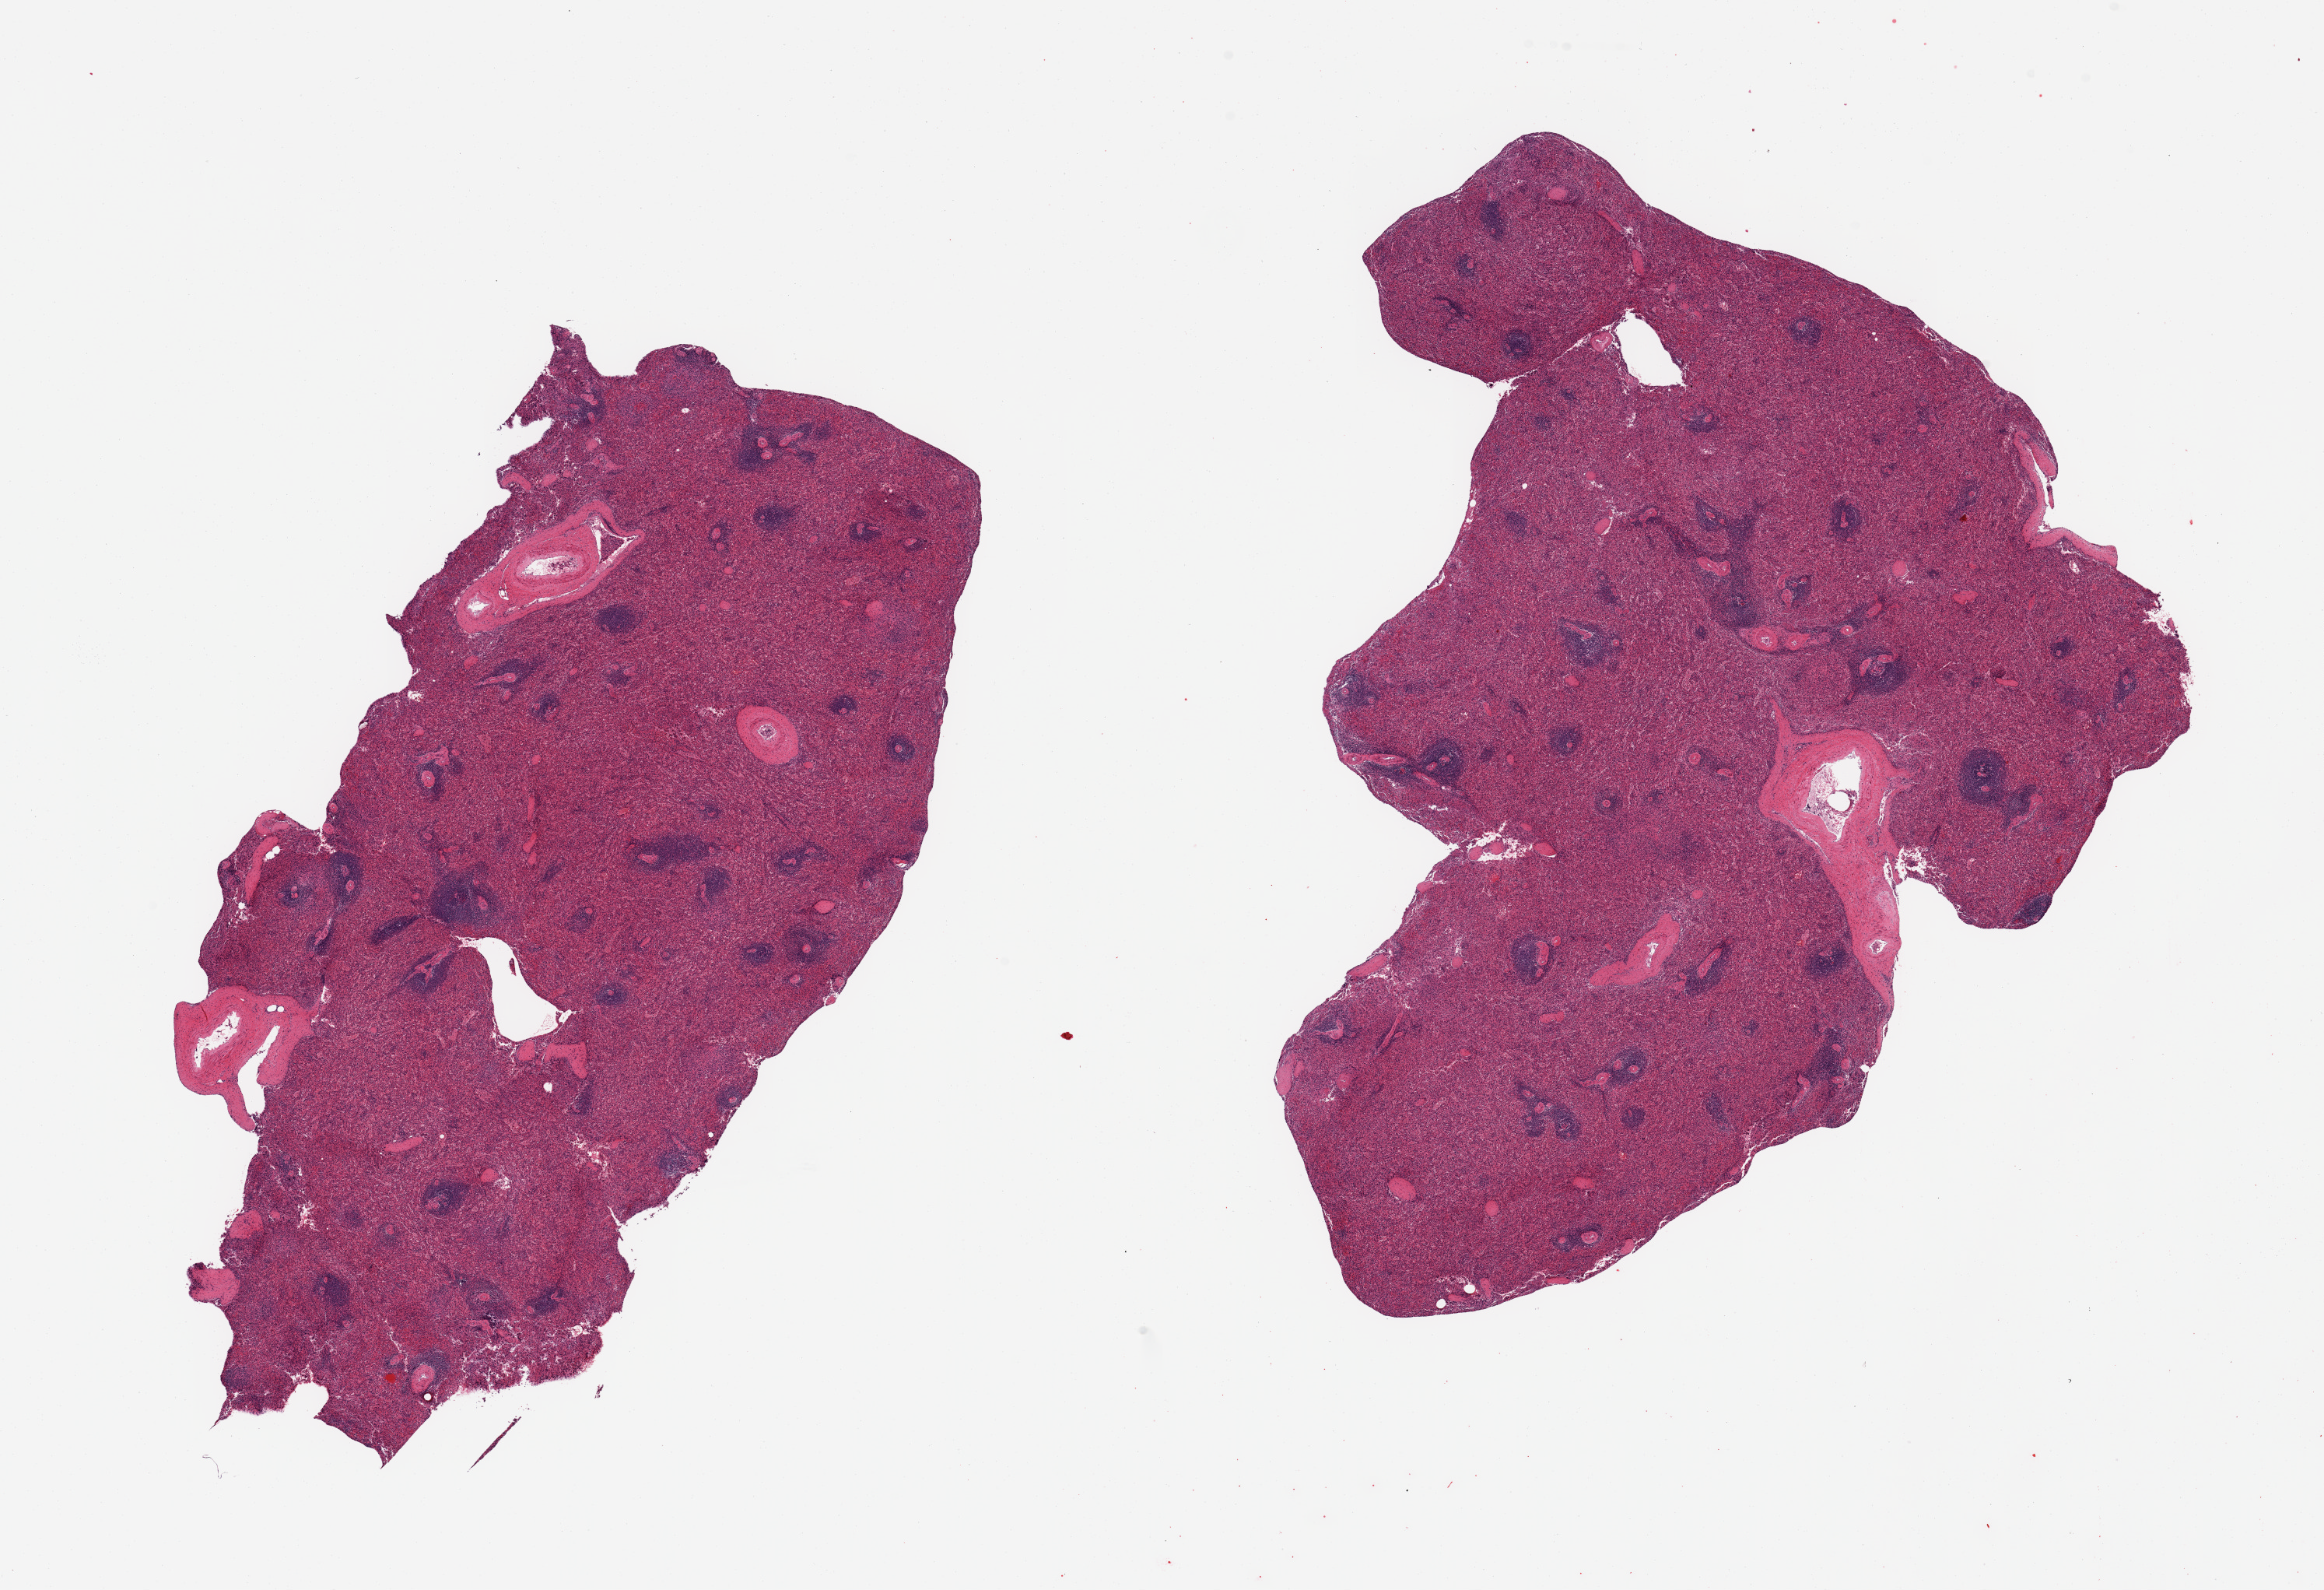
Digitized hematoxylin and eosin (H&E)-stained section, a low-resolution overview of the entire scanned area, about 23.6 x 16.2 mm; PAXgene-fixed paraffin-embedded (PFPE) section; sampled site (target tissue): spleen; tissue donor sample. Male donor.
* review note (as recorded): 2 pieces, no abnormalities